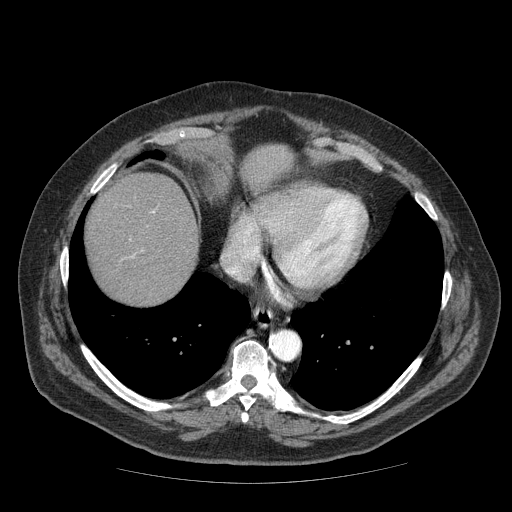
Contrast-enhanced abdominal CT (liver protocol), one axial slice; position 65 of 85 along the scan axis; soft-tissue window (W 400 / L 40 HU); 512 × 512 image matrix, field of view 420 × 420 mm. Case-level facts recorded for this patient, not image findings: diagnosis: hepatocellular carcinoma (patient treated with transarterial chemoembolisation; whether this scan precedes or follows treatment is not stated here); TNM stage (as recorded): Stage-IIIA; Child-Pugh class: A; tumour nodularity: multinodular.
Structures marked on this image (semi-automatically segmented with operator editing):
- liver parenchyma outside the tumour (the mass and vessels are separate outlines, so this box may not span the whole liver): bounding box [x1, y1, x2, y2] px = [86, 146, 291, 304]